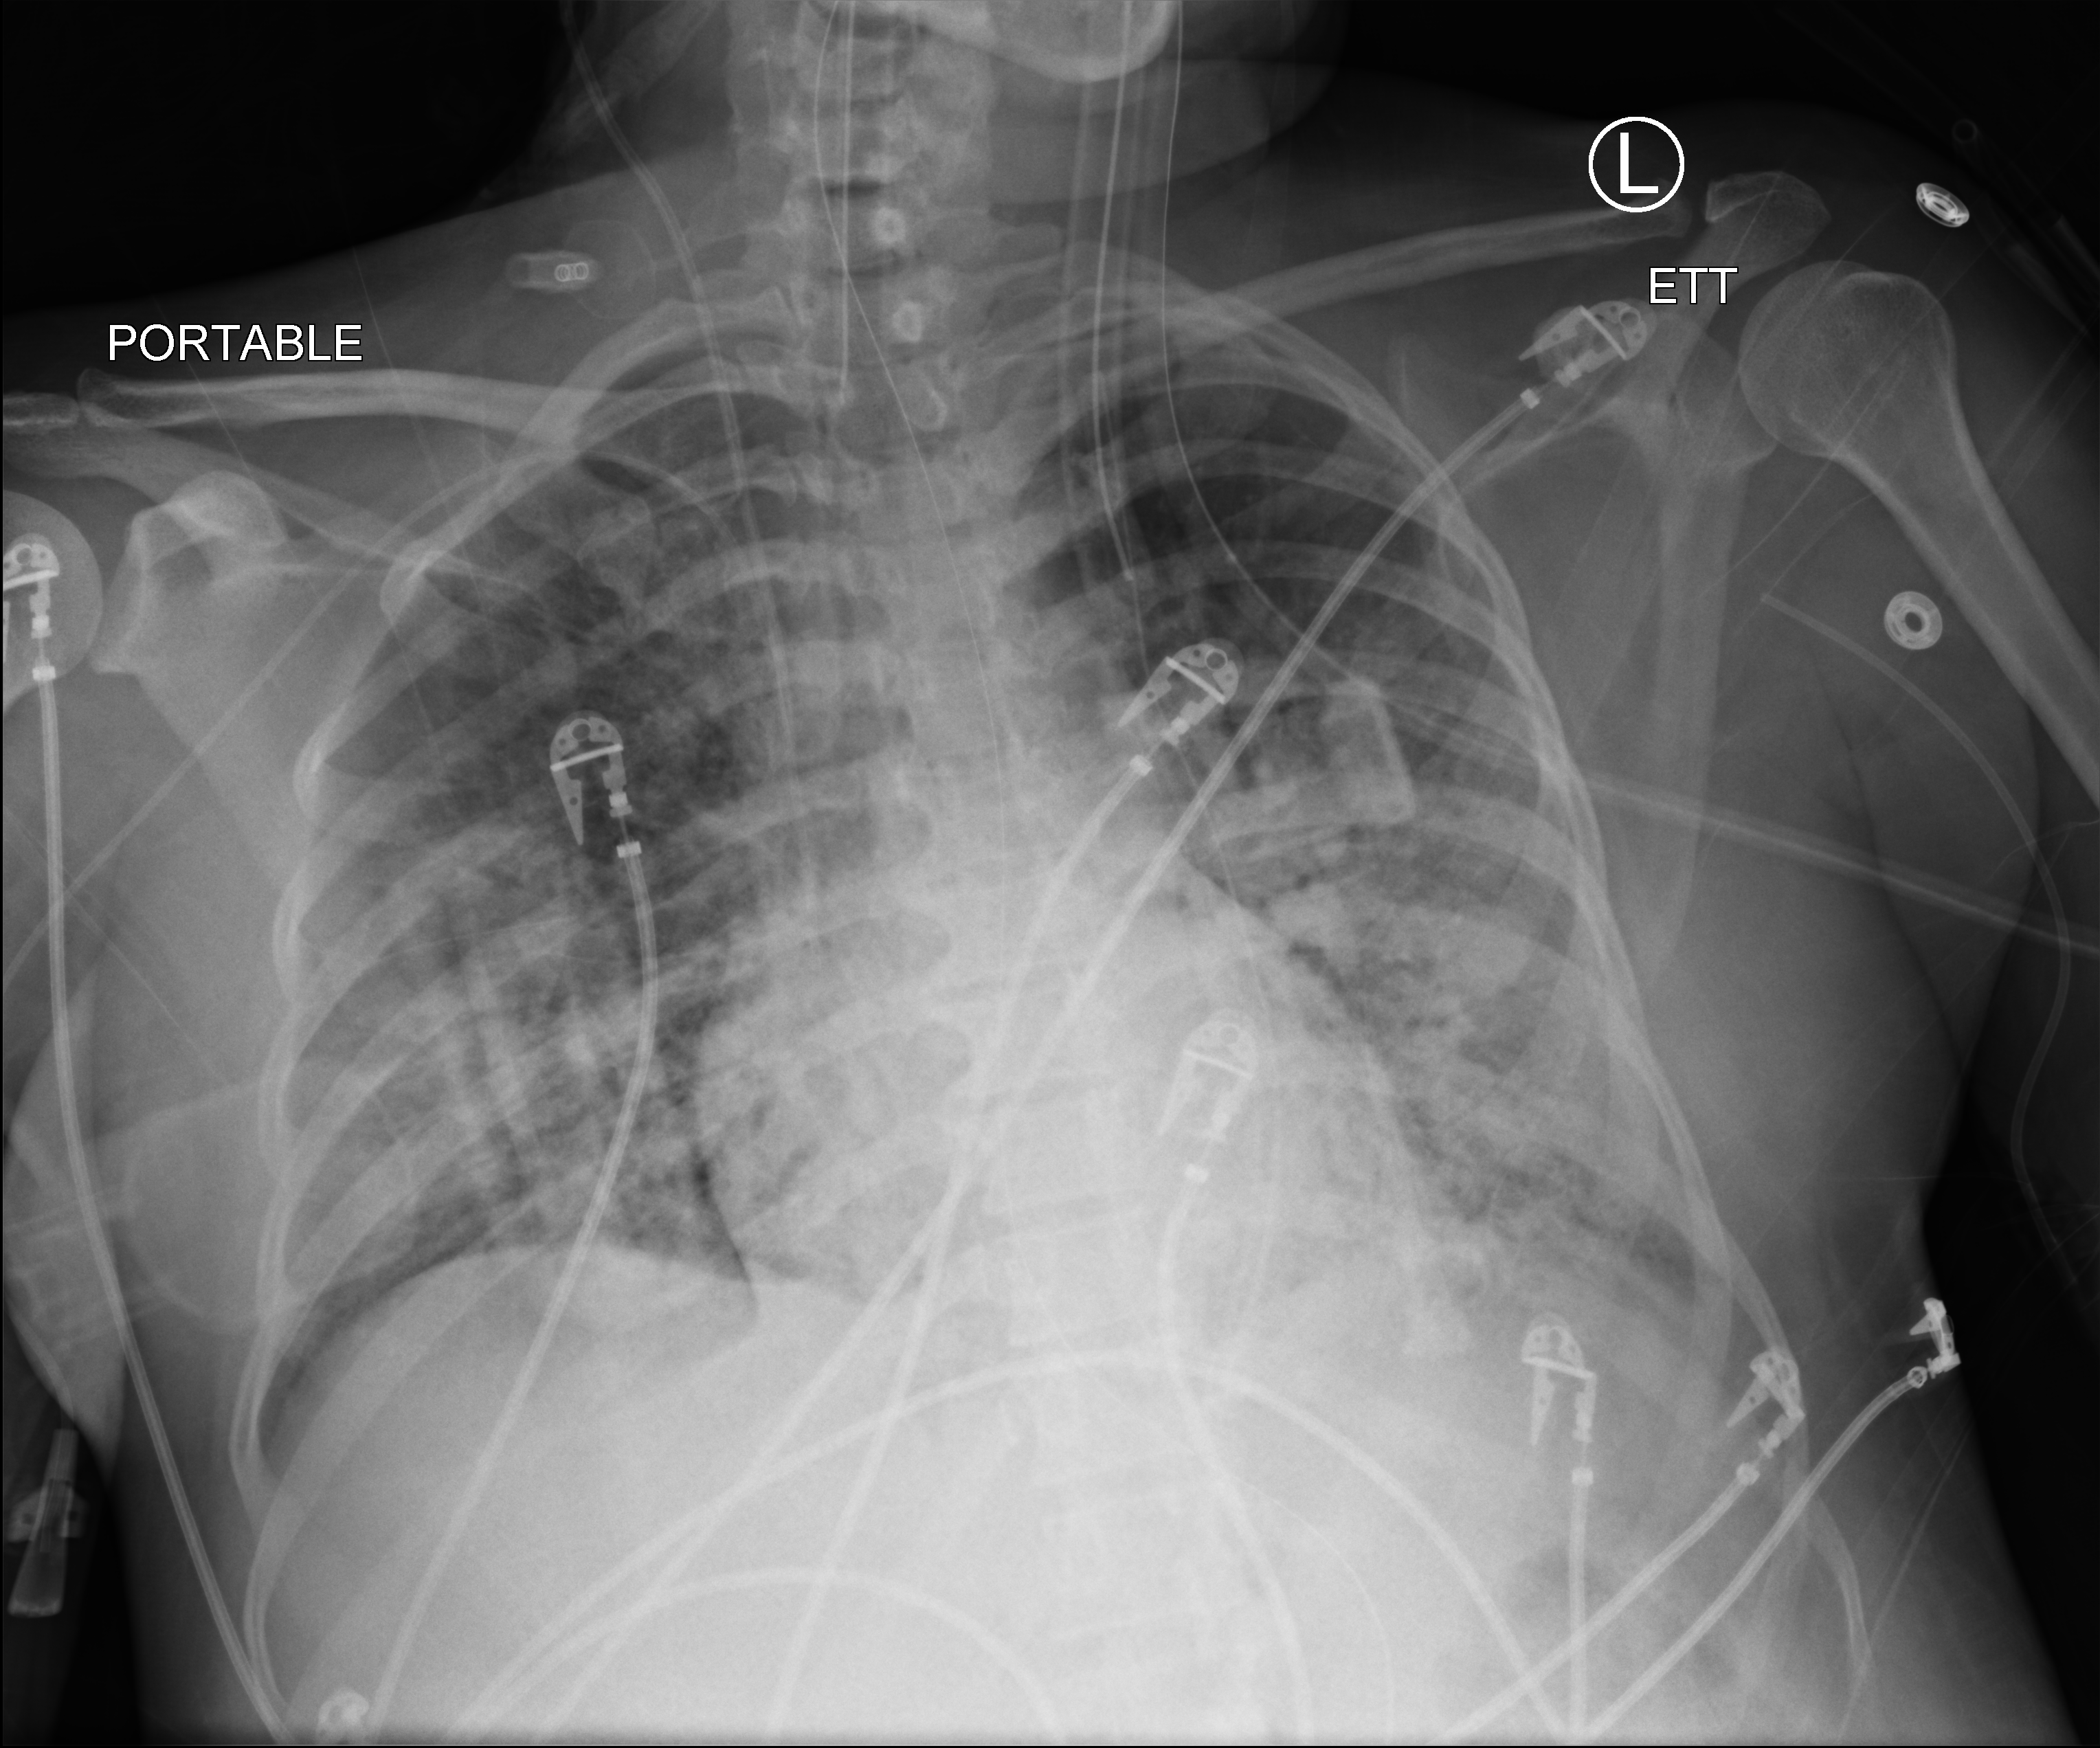
Bedside chest radiograph (computed radiography). Female patient hospitalised with COVID-19, age 18–59 years.
Hospital-stay facts (about this admission, not read from this image; timing relative to this image not recorded): chronic kidney disease (admission record): no; length of hospital stay: 71 days; admitted to intensive care during this hospital stay: yes.